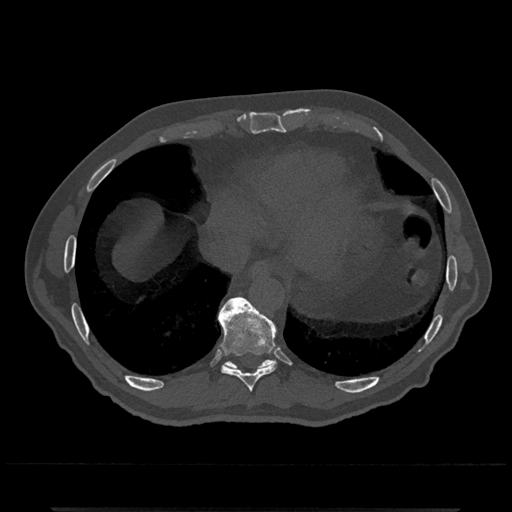
CT including the spine, one axial slice; position 596 of 797 along the scan axis; reconstruction kernel Br40s/3; 120 kVp; bone window (W 1800 / L 400 HU); 0.5 mm slice thickness; 512 × 512 image matrix. Male patient, age 67 years. From the clinical record (not read from this slice): primary cancer: prostate.
Outlined on this slice (semi-automatic segmentation, software-assisted and operator-edited):
- T10 vertebra: box from (x=224, y=297) to (x=276, y=368) px
- T9 vertebra: (x=218, y=297)–(x=278, y=392)